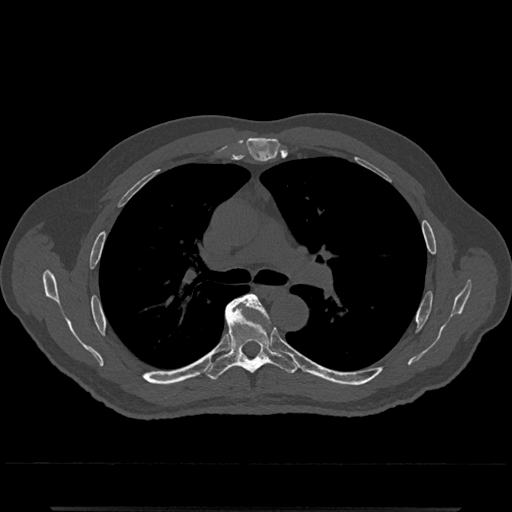
CT including the spine, one axial slice. Position 786 of 797 along the scan axis. 120 kVp. Bone window (W 1800 / L 400 HU). 512 × 512 image matrix, field of view 393 × 393 mm. Male patient, age 67 years. Case-level facts recorded for this patient, not image findings: primary cancer: prostate.
Annotated regions visible in this slice (semi-automatically segmented with operator editing):
- T5 vertebra: bounding box (x1, y1, x2, y2) in pixels: (235, 294, 268, 317)
- T6 vertebra: (205, 299, 298, 380)